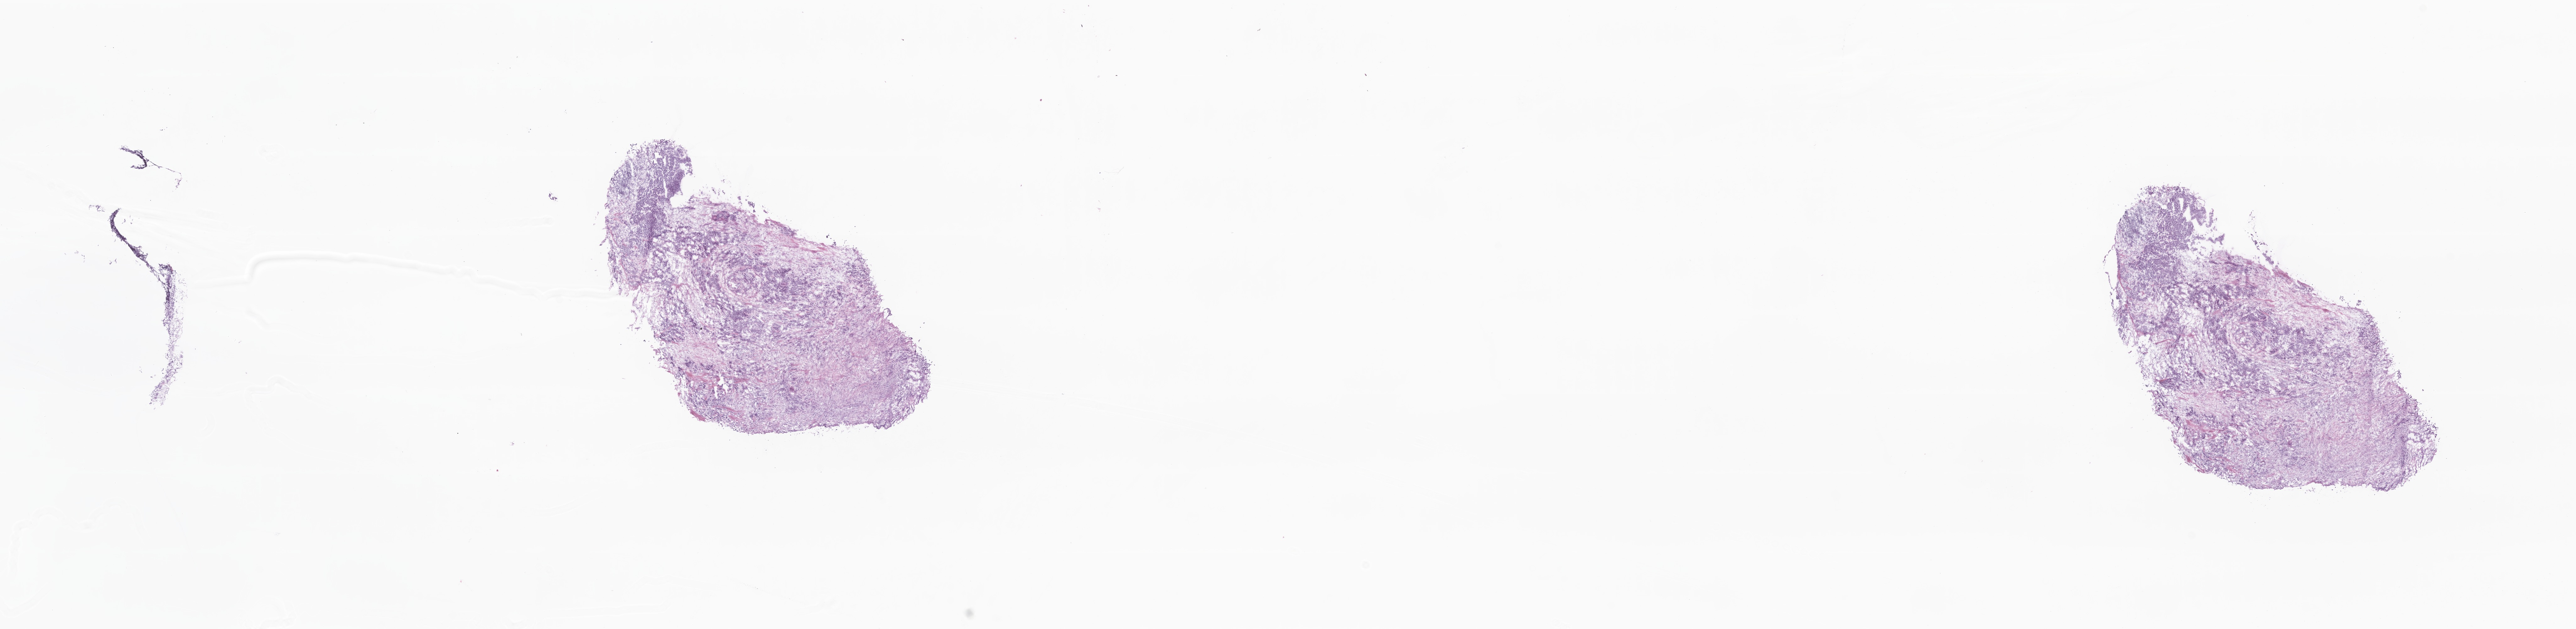
Digitized hematoxylin and eosin (H&E)-stained section — a low-resolution overview of the entire scanned area, about 34.6 x 8.5 mm; cryosection; primary tumor; anatomic site: breast (right). Female, age 79 years at initial diagnosis. Composition of this section per pathologist review: tumor cells 100%, tumor nuclei 75%, stromal cells 0%, necrosis 0%, normal cells 0%. Inflammatory infiltration, as recorded: lymphocyte infiltration 0%, monocyte infiltration 0%, neutrophil infiltration 0%.
Histologic diagnosis: Lobular carcinoma, NOS. Section: bottom of the tissue portion.